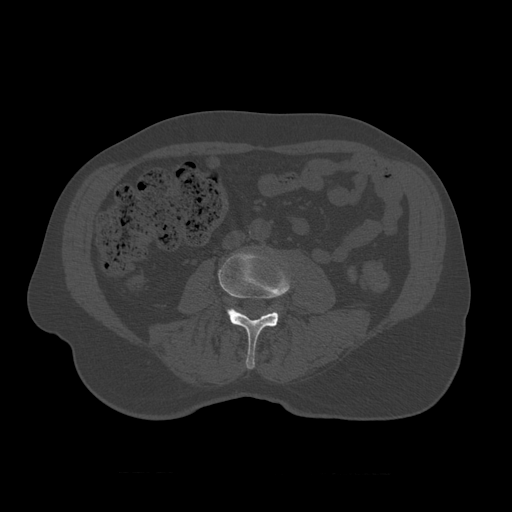
CT including the spine, one axial slice; slice 297 of 450 in the series (ordered by position); reconstruction kernel STANDARD; 120 kVp; bone window (W 1800 / L 400 HU); 512 × 512 image matrix. Patient age 75 years. Case-level facts recorded for this patient, not image findings: primary cancer: prostate.
Annotated regions visible in this slice (semi-automatic segmentation, software-assisted and operator-edited):
- L3 vertebra: box from (x=218, y=251) to (x=292, y=370) px
- L4 vertebra: (x=231, y=307)–(x=282, y=310)